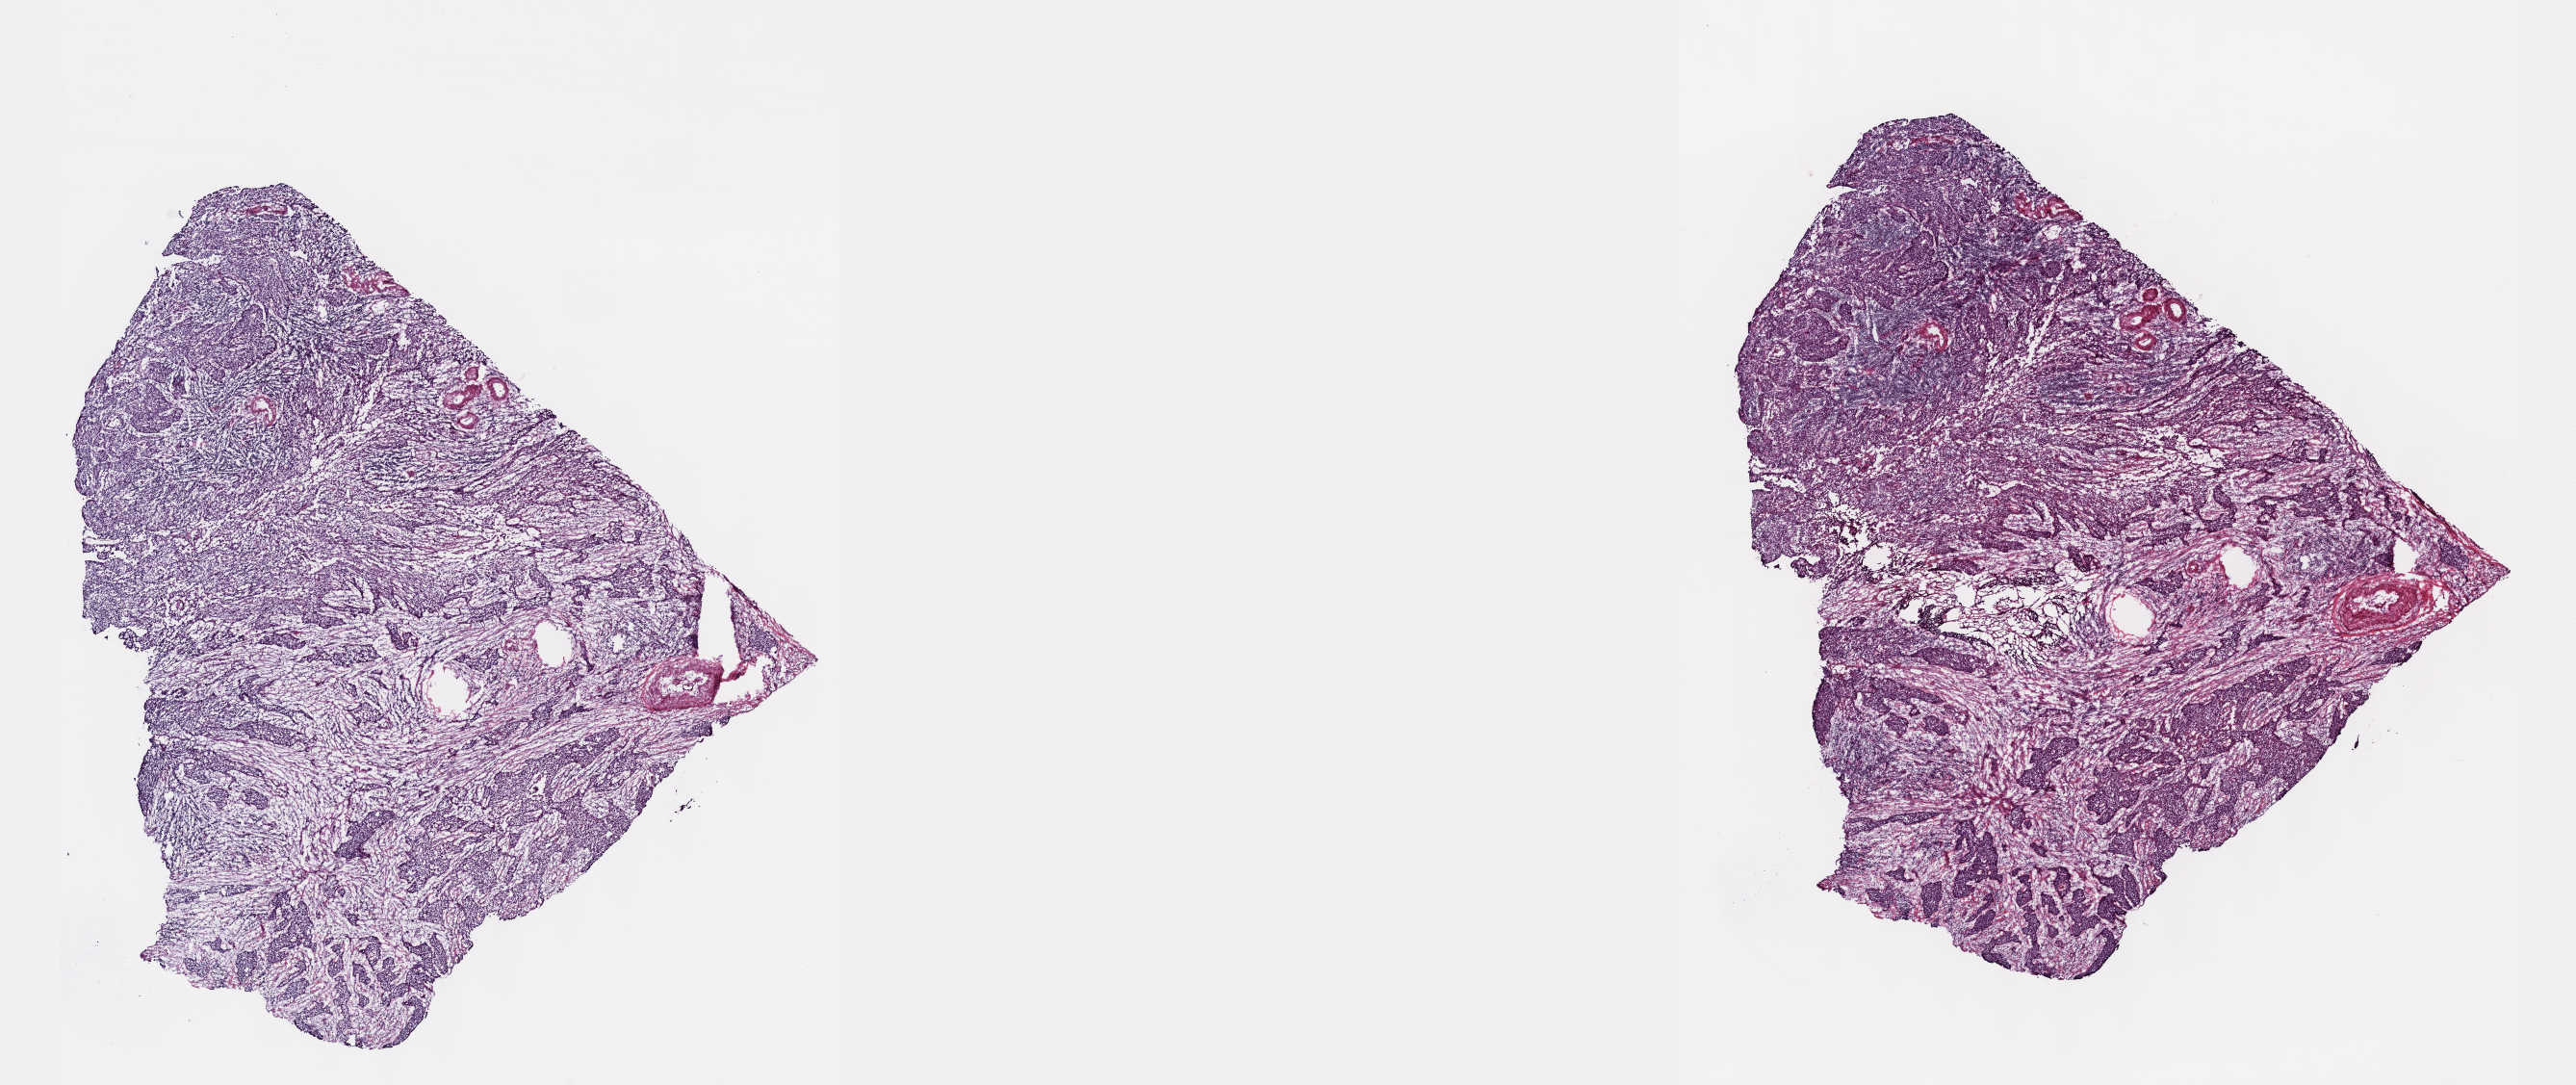
Whole-slide histology image, H&E, low-resolution overview of the scanned area, about 21.6 x 9.1 mm, frozen section from the top of the tissue portion, cervix, primary tumour sample. Female, age 46 years at initial diagnosis. Histologic grade: G2 (moderately differentiated). Slide review estimates, as recorded: tumour cells 70%, tumour nuclei 70%, normal cells 10%, stromal cells 20%, necrosis 0%. Infiltration values recorded for this section: lymphocyte infiltration 10%, monocyte infiltration 0%, neutrophil infiltration 0%.
• diagnosis: Squamous cell carcinoma, large cell, nonkeratinizing, NOS (cervix uteri)
• FIGO stage: IB1